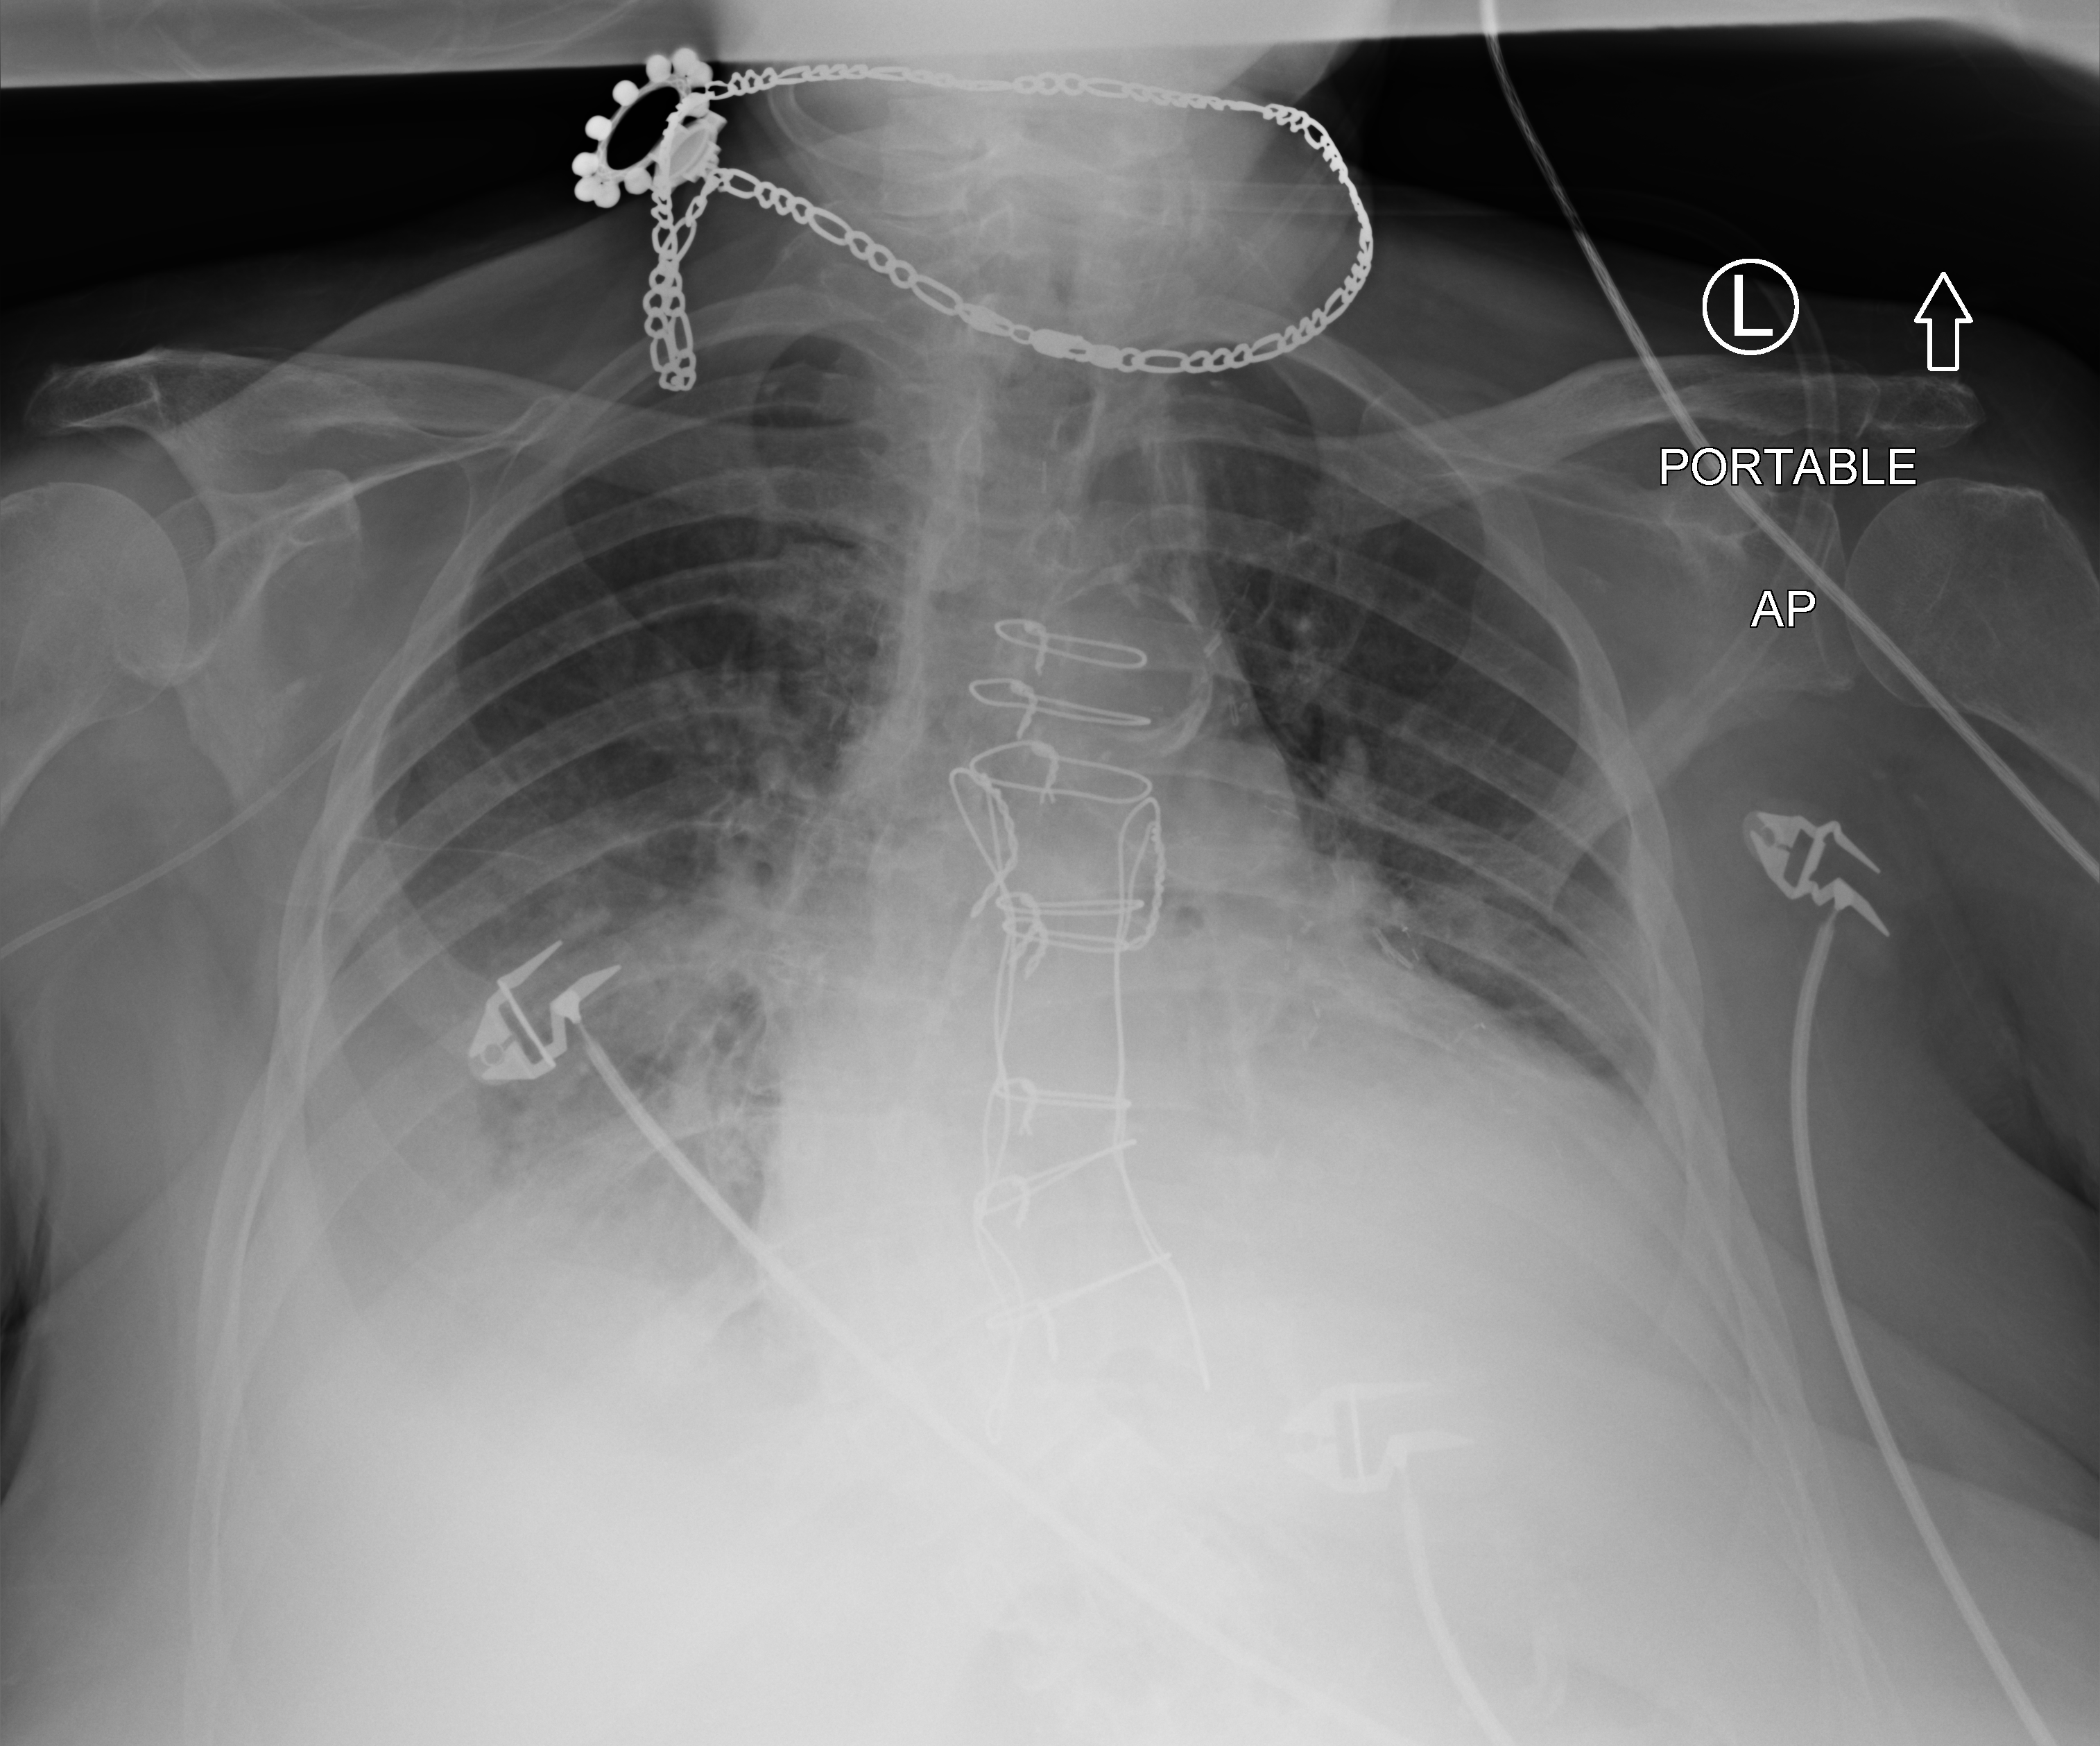
Bedside chest radiograph (computed radiography); anteroposterior (AP) projection. Patient hospitalised with COVID-19; female, aged 75–90 years.
From the hospital-stay record, not from the radiograph (when in the stay this image was taken is not recorded): mechanically ventilated during this hospital stay: no; length of hospital stay: 10 days; admitted to intensive care during this hospital stay: no.